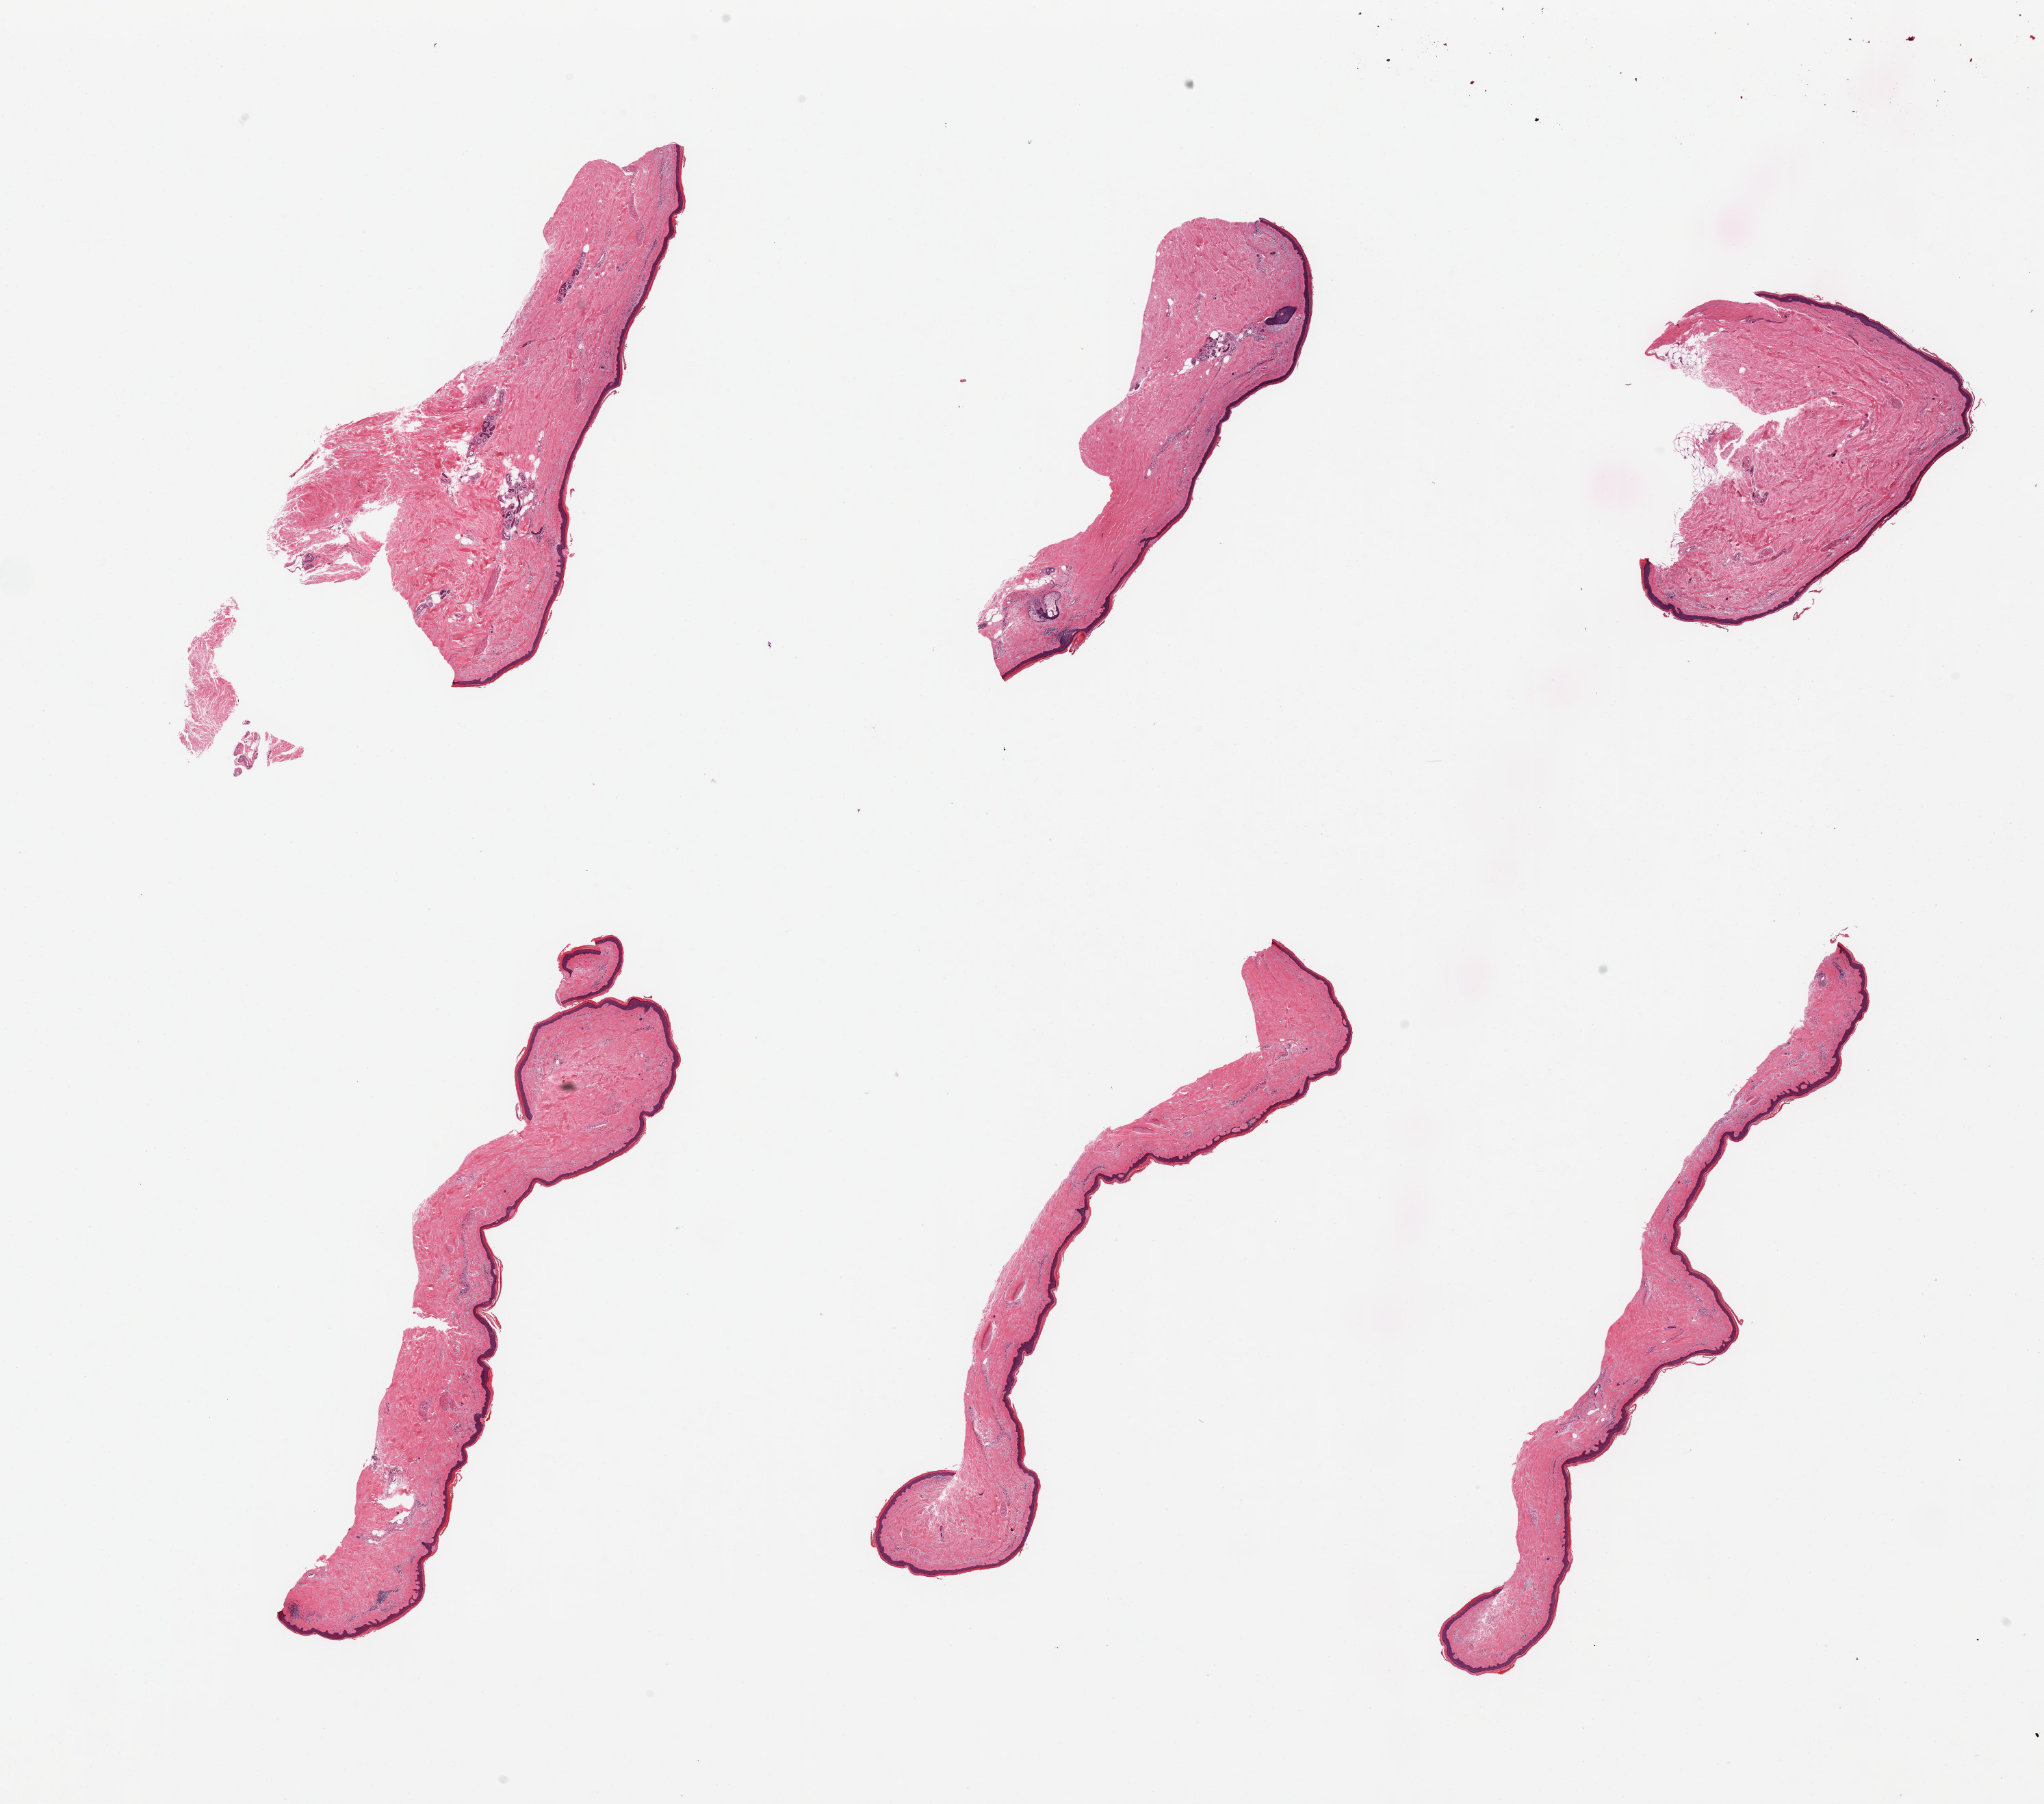
Whole-slide image, haematoxylin and eosin stain, brightfield, whole scanned area (about 23.6 x 20.9 mm) shown as a low-resolution overview; PAXgene-fixed, paraffin-embedded tissue; section of skin of lower leg (target tissue); tissue donor sample.
* pathologist's review note for this sample: 6 pieces, no dermal fat; squamous epithelium is ~50-60 microns